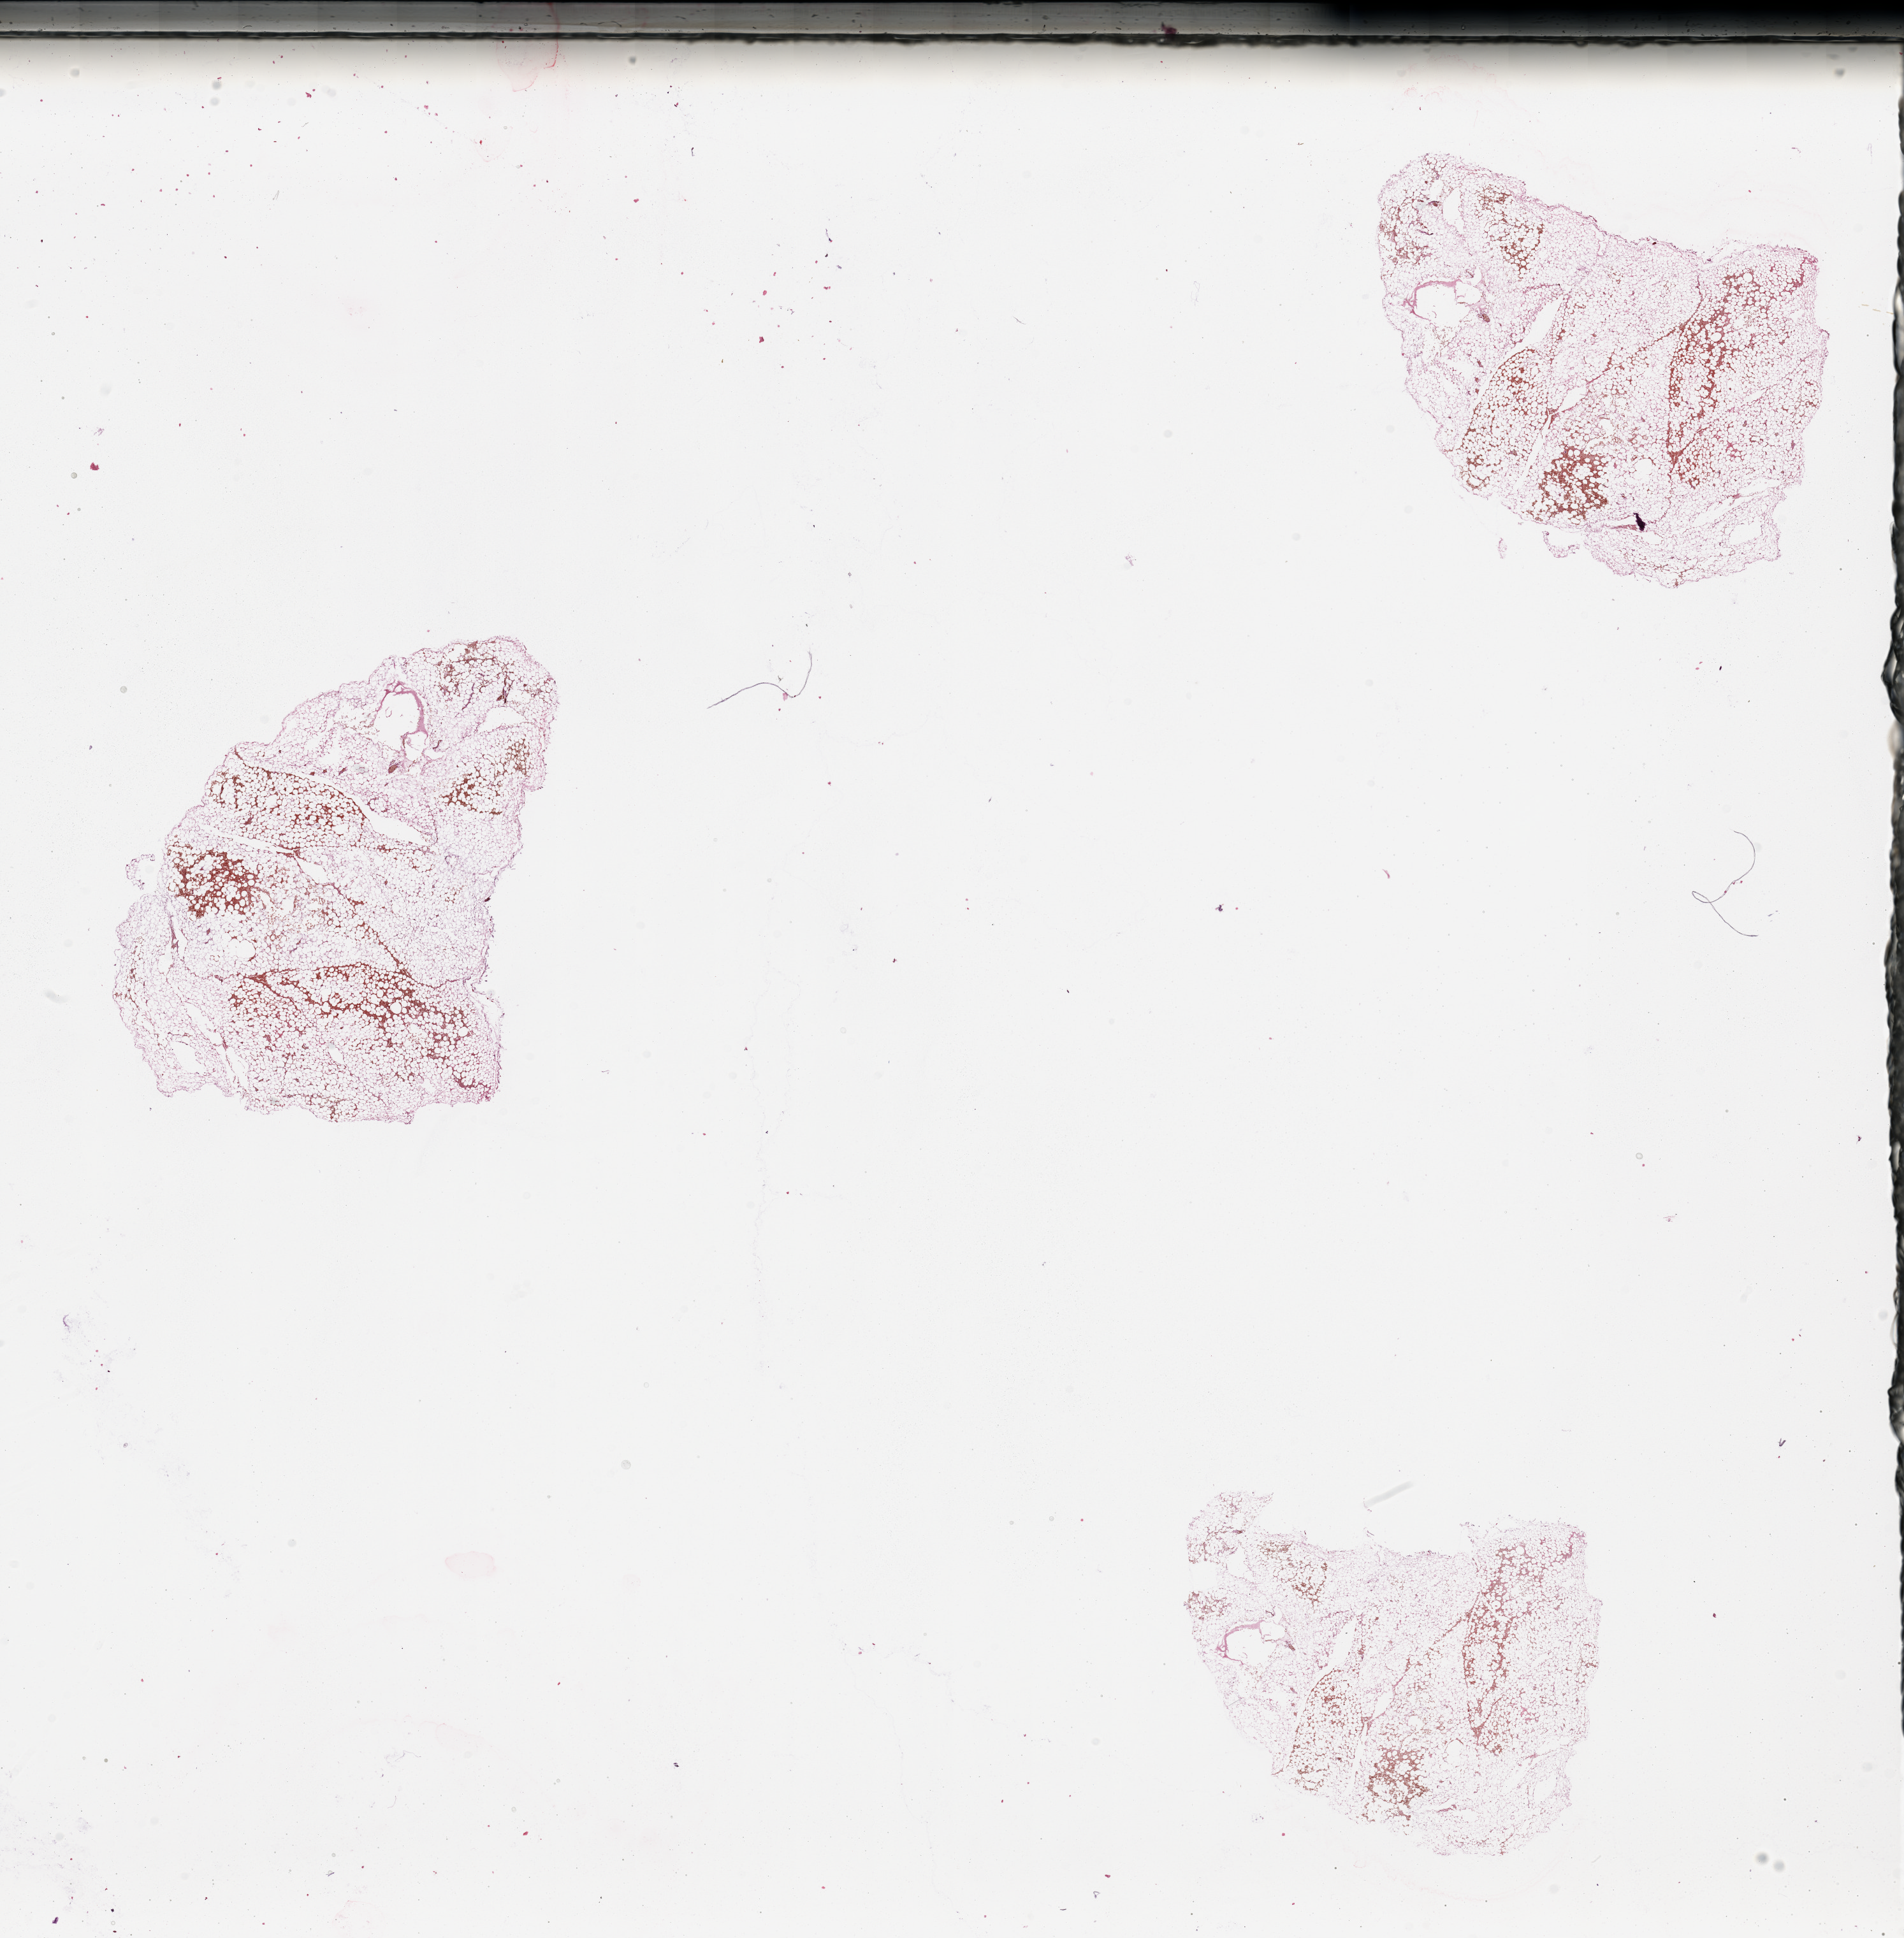
Digitized Hematoxylin and eosin (H&E) stained tissue section (whole slide), a low-resolution overview of the entire scanned area, about 23.6 x 24.1 mm (slide scanned at 20x); normal (non-tumour) tissue sample, sampled site: lymph node. 32-year-old male patient.
This section: normal (non-tumour) tissue from the same patient. Patient diagnosis: Malignant melanoma, NOS.